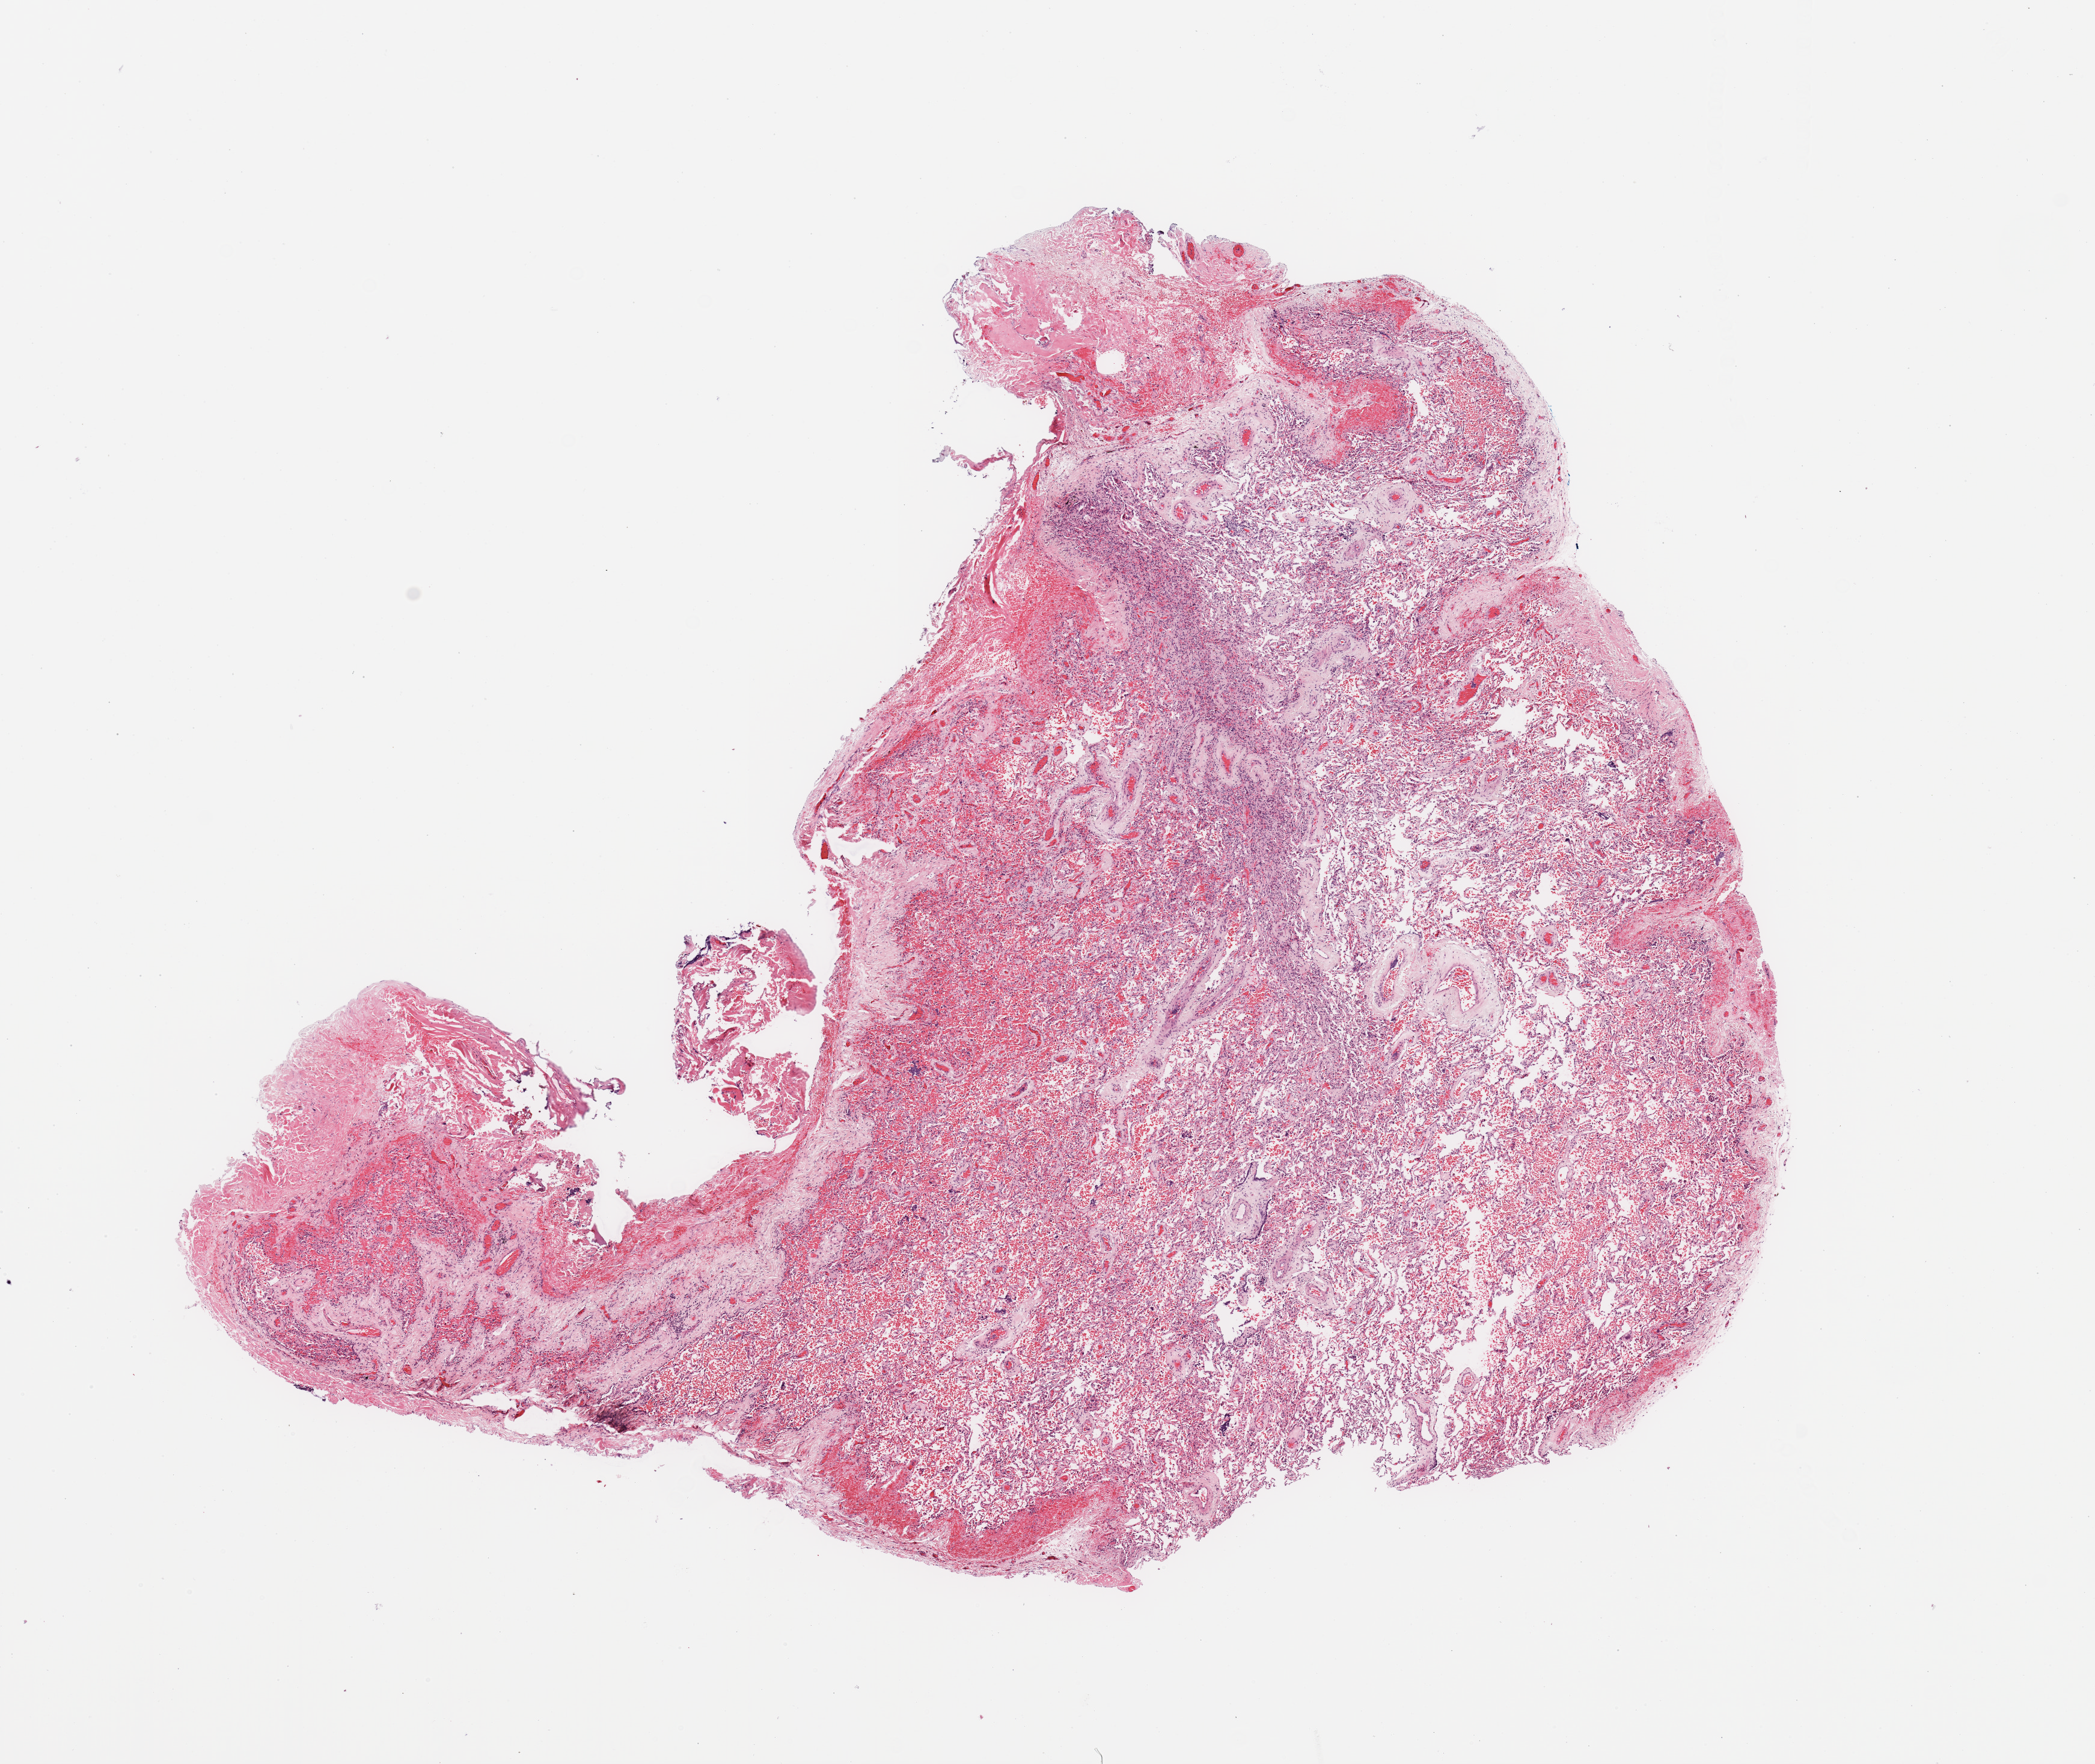
Digitized Hematoxylin and eosin (H&E) stained tissue section (whole slide) — a low-resolution overview of the entire scanned area, about 13.8 x 11.6 mm (slide scanned at 20x); normal (non-tumour) tissue sample, sampled site: lung. 71-year-old male patient.
* this section: normal (non-tumour) tissue from the same patient
* patient diagnosis: Squamous cell carcinoma, NOS